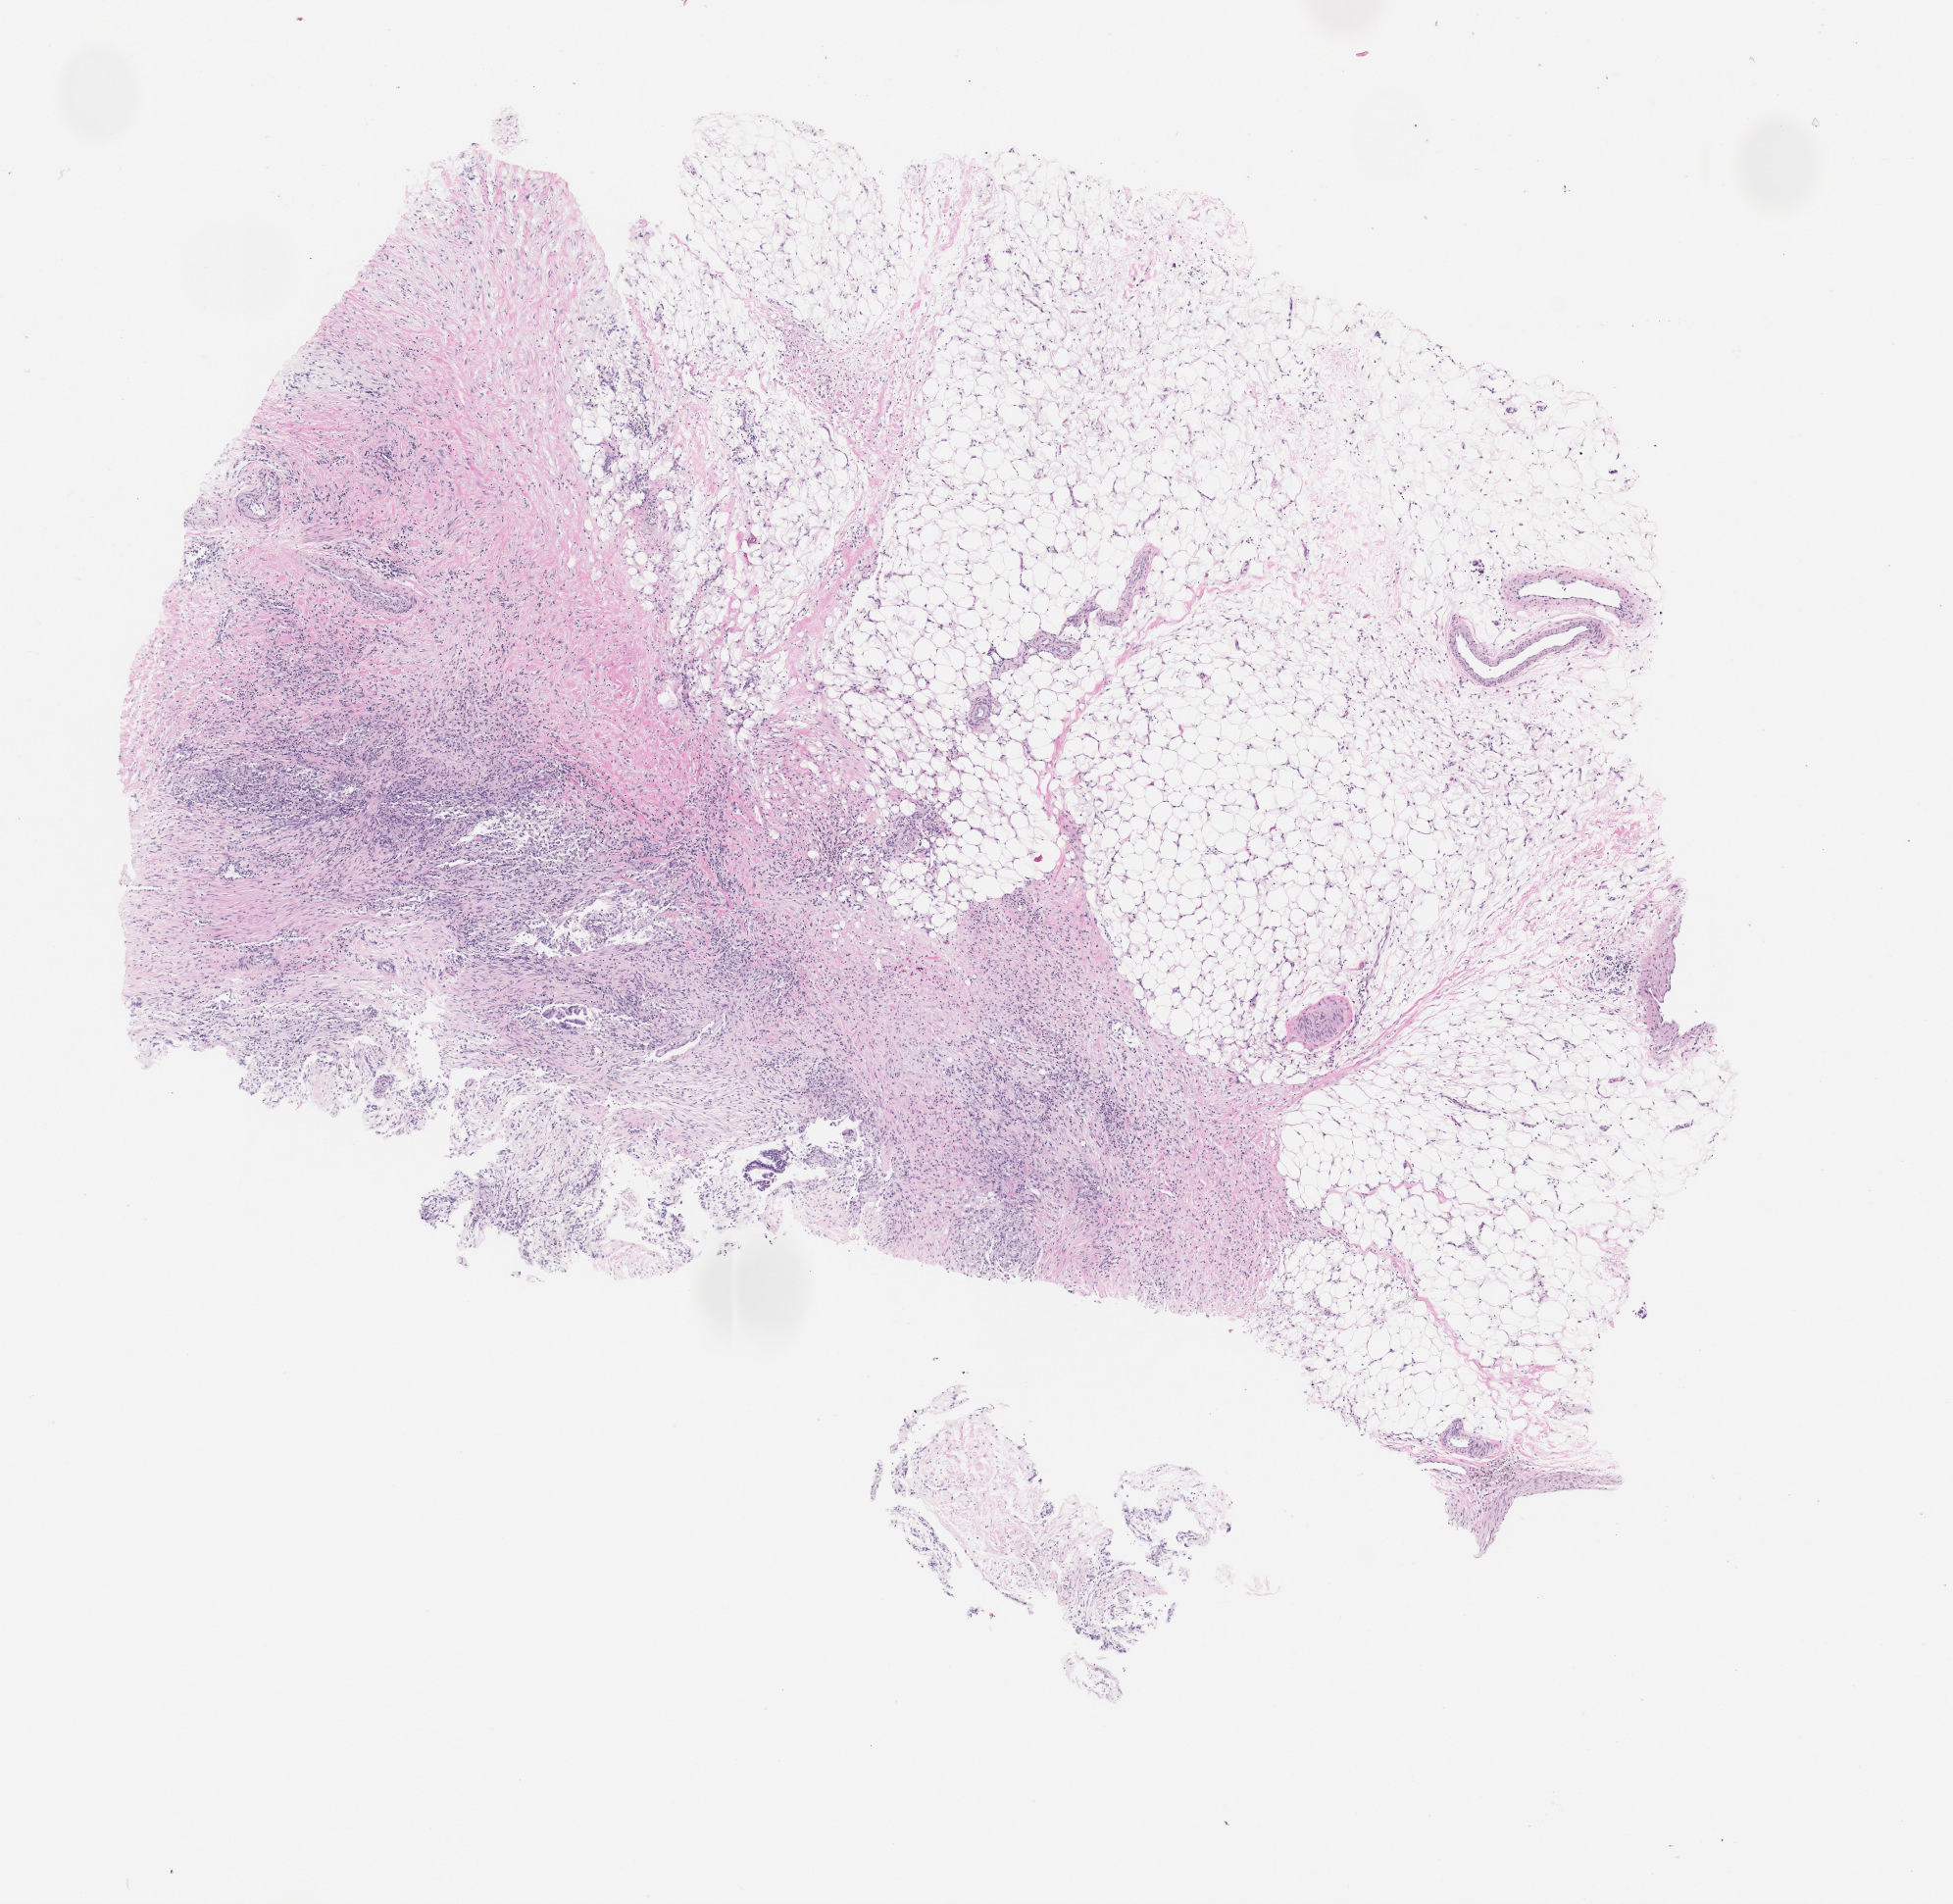
Hematoxylin and eosin (H&E) whole-slide image of the patient's (originator) tumor tissue, low-resolution overview of the scanned area, about 8.0 x 7.8 mm; formalin-fixed, paraffin-embedded (FFPE) tissue; originating tumor site category: colon. Patient: male, age 75 years.
Diagnosis: Colon Adenocarcinoma.